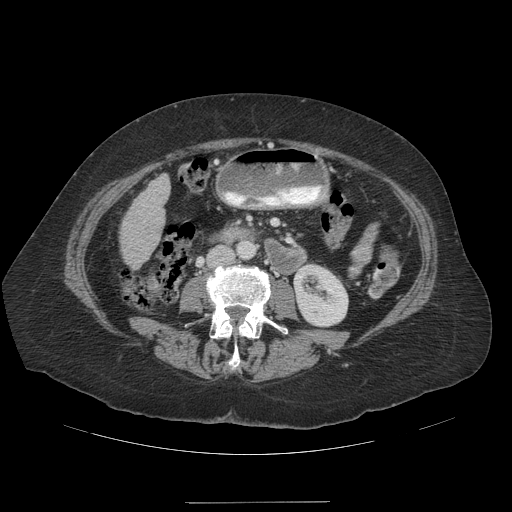
Contrast-enhanced abdominal CT (liver protocol), one axial slice. Slice 33 of 99 in the series (ordered by position). Soft-tissue window (W 400 / L 40 HU). 2.5 mm slice thickness. 512 × 512 image matrix, field of view 440 × 440 mm. From the clinical record (not read from this slice): diagnosis: hepatocellular carcinoma (patient treated with transarterial chemoembolisation; whether this scan precedes or follows treatment is not stated here); TNM stage (as recorded): Stage-IVA; Child-Pugh class: A; tumour nodularity: multinodular.
Annotated regions visible in this slice (semi-automatic segmentation, software-assisted and operator-edited):
- liver parenchyma outside the tumour (the mass and vessels are separate outlines, so this box may not span the whole liver): bounding box <120,174,170,268> (left, top, right, bottom; pixels)